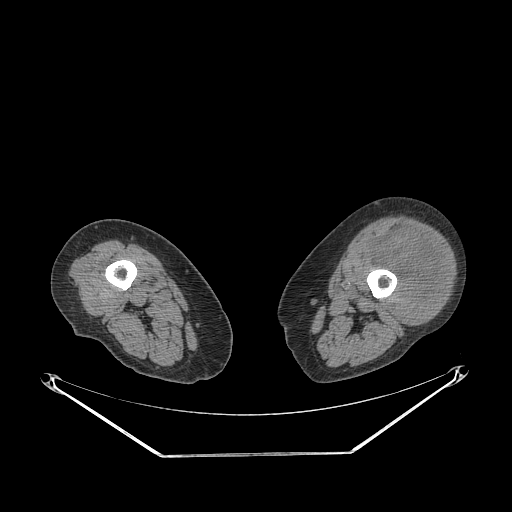
CT of an extremity soft-tissue mass (from a PET/CT study), one axial slice. Position 211 of 267 along the scan axis. 140 kVp. Soft-tissue window (W 400 / L 40 HU). 512 × 512 image matrix, field of view 500 × 500 mm. Female patient. Case-level facts recorded for this patient, not image findings: histological type: undifferentiated – high grade; grade: high; site of the primary tumour: left thigh.
Annotated regions visible in this slice (expert contour drawn on MRI and transferred to this co-registered scan by the dataset authors):
- gross tumour volume including surrounding oedema: box from (x=365, y=230) to (x=449, y=323) px
- gross tumour volume (mass): (x=374, y=231)–(x=446, y=323)